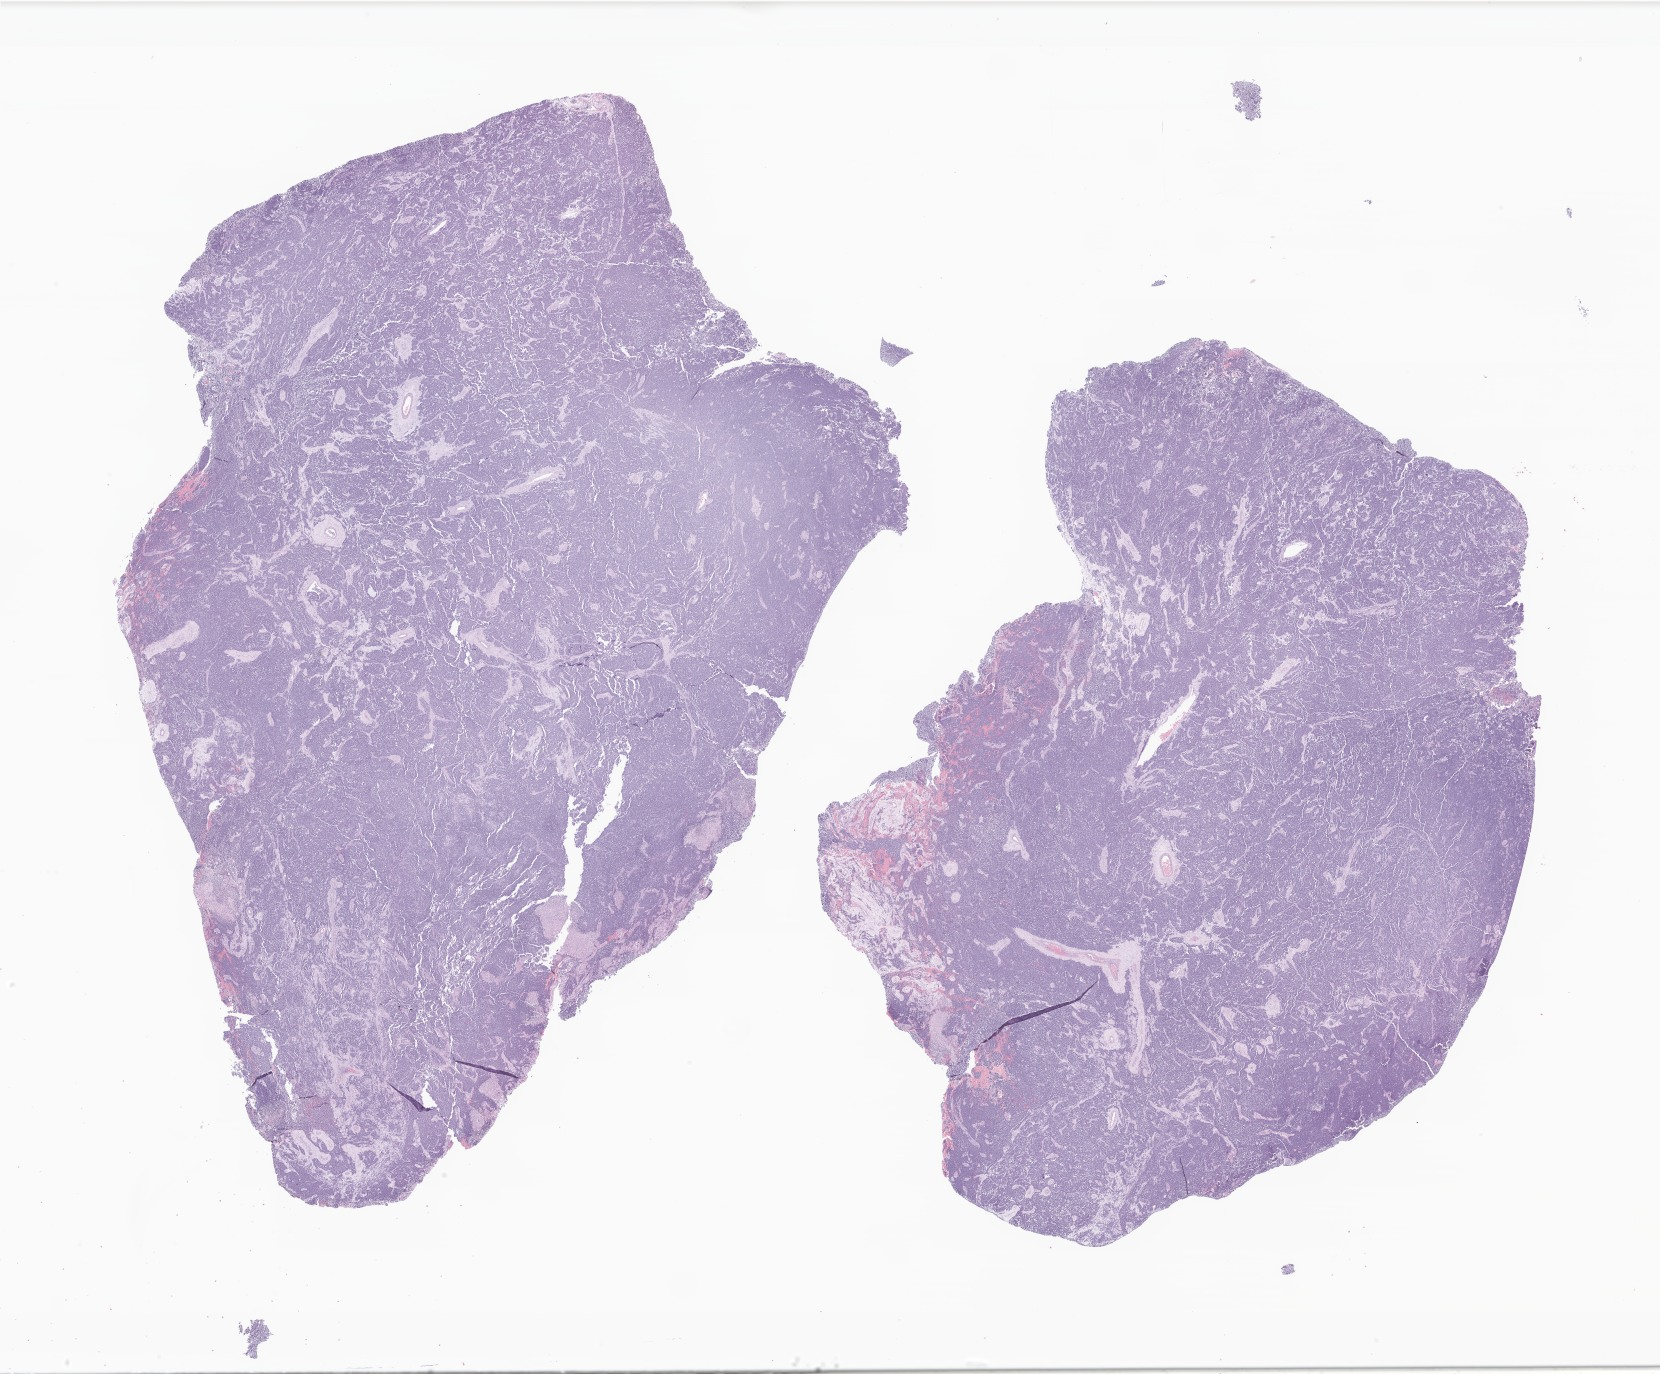
Digitized haematoxylin and eosin-stained section of tumor tissue from the cerebellum — a low-resolution overview of the entire scanned area, about 28.0 x 23.2 mm. Formalin-fixed paraffin-embedded section. Patient female; age 512 days (about 1.4 years).
Diagnosis (ICD-O-3 morphology term): Medulloblastoma, NOS.